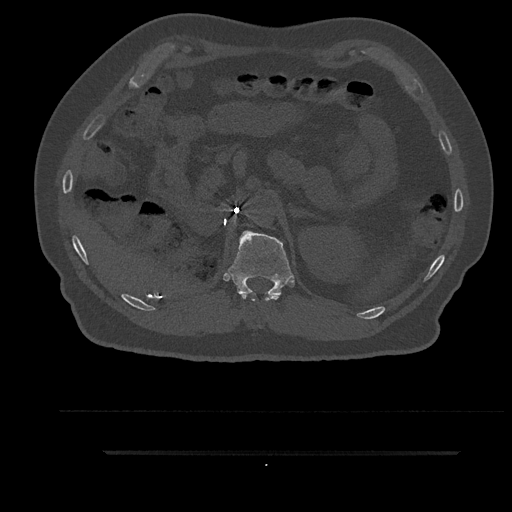
CT including the spine, one axial slice; slice 261 of 797 in the series (ordered by position); reconstruction kernel Br40s/3; 120 kVp; bone window (W 1800 / L 400 HU); 0.5 mm slice thickness; 512 × 512 image matrix, field of view 432 × 432 mm. Patient: male, 63 years. Case-level facts recorded for this patient, not image findings: primary cancer: renal; vertebrae with lytic lesions (as recorded): T8.
Outlined on this slice (semi-automatic segmentation, software-assisted and operator-edited):
- T11 vertebra: bounding box <241,294,281,301> (left, top, right, bottom; pixels)
- T12 vertebra: <227,230,294,296>